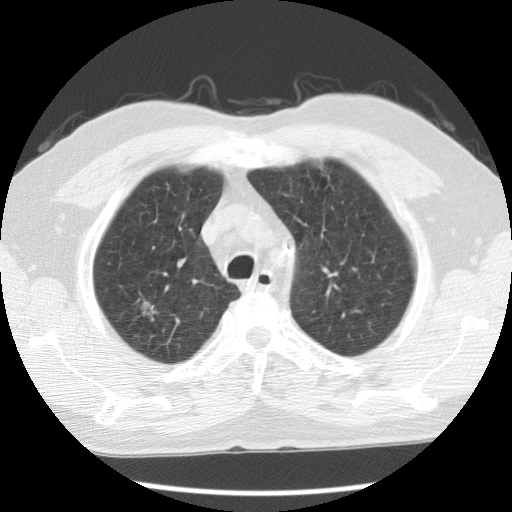
Low-dose screening chest CT, axial slice; first (baseline) screen; lung window (W 1500 / L -600 HU); 2.5 mm slice thickness; slice 88 of 110 in the series. Male, age 68 years at enrolment.
• Lesion marked by an expert reader, box from (x=131, y=295) to (x=170, y=332) px.
• Reader record for this screening exam (exam-level; its link to the box is not recorded): non-calcified nodule or mass ≥4 mm, right upper lobe, 9 × 7 mm, poorly defined margins, ground glass attenuation.
• Later outcome: lung cancer diagnosed 410 days after this screen — adenocarcinoma, NOS, right upper lobe, moderately differentiated (G2), stage IA (AJCC 6th edition), 28 mm at pathology.